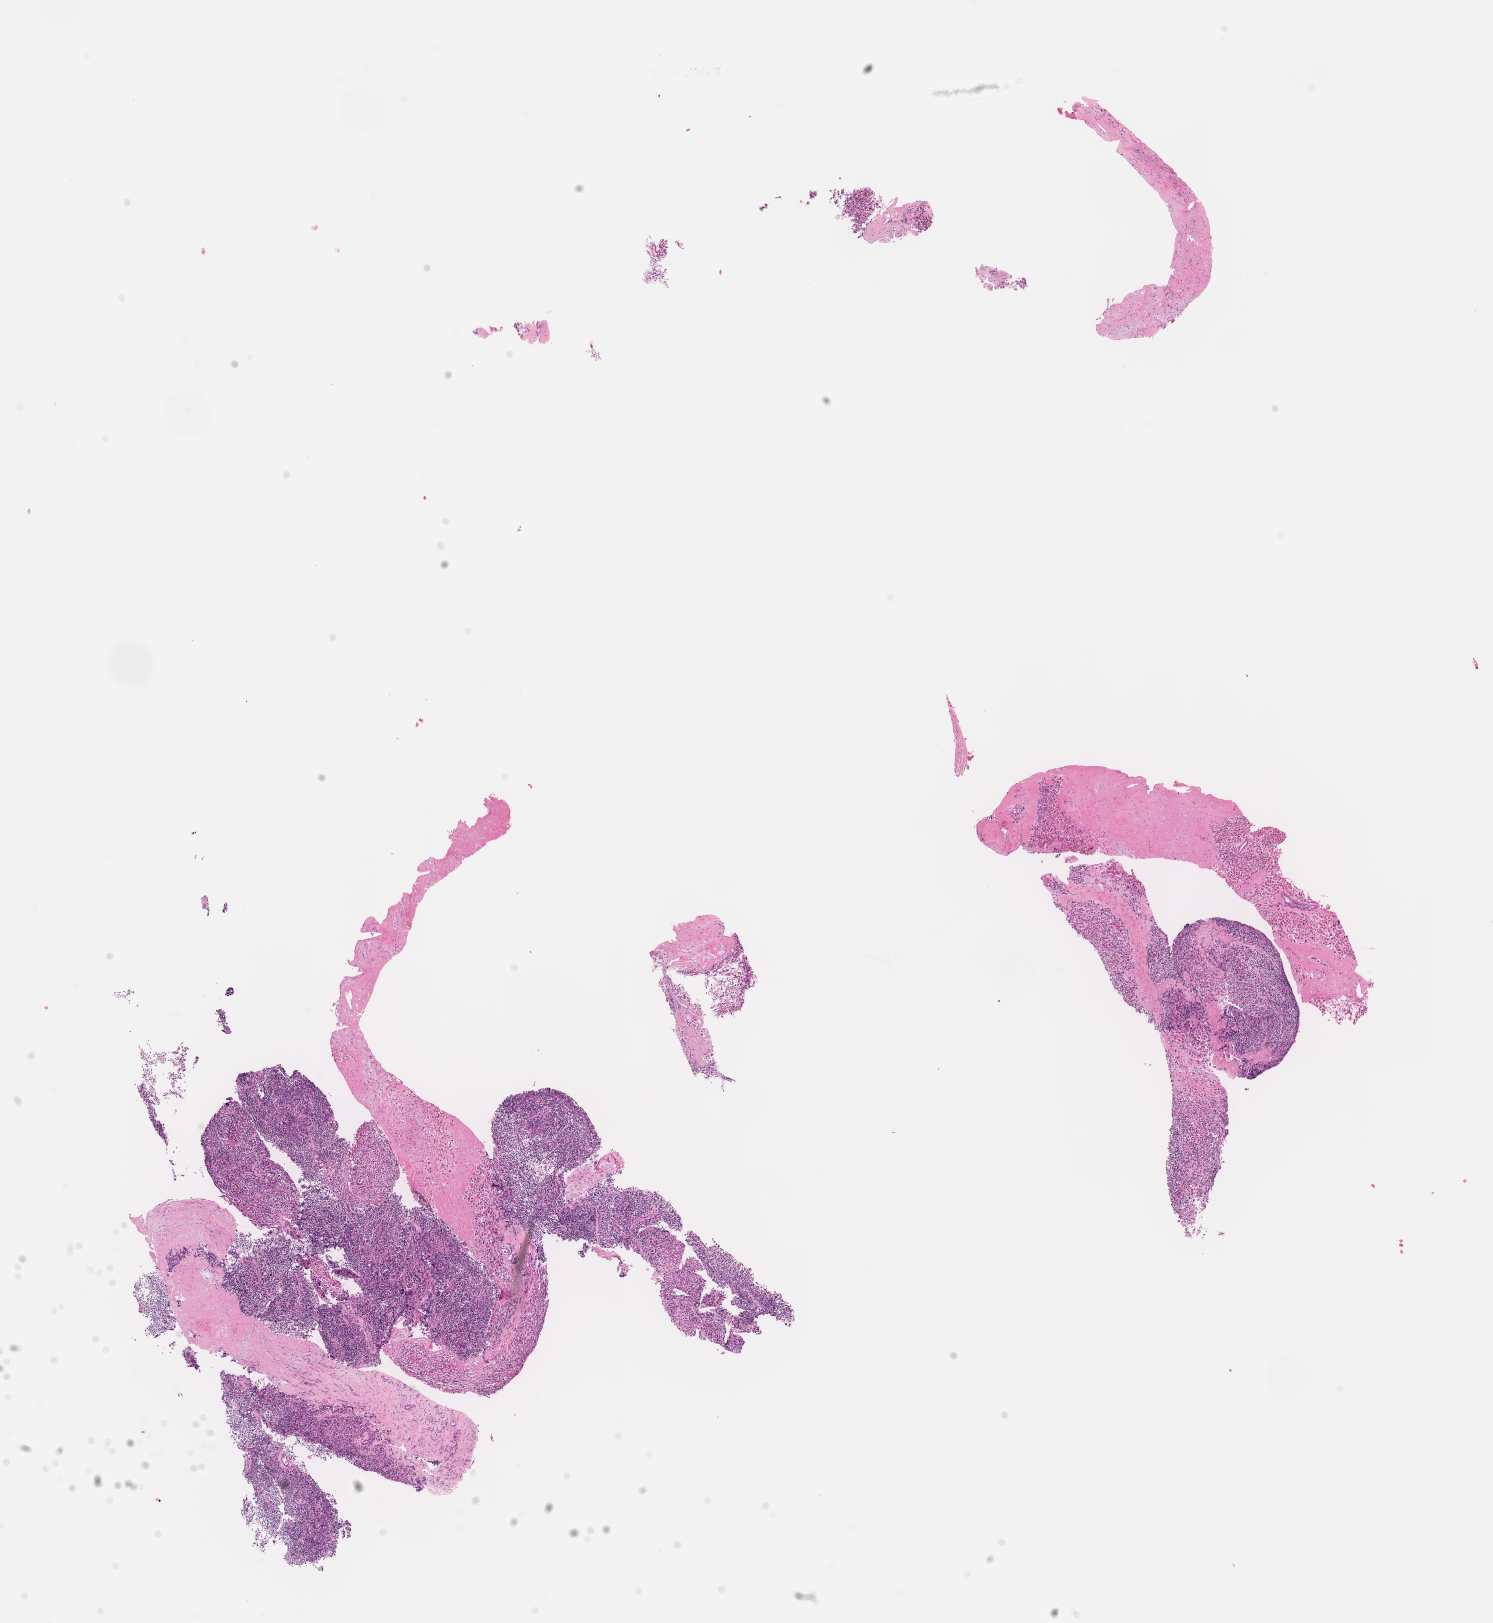
Digitized H&E-stained section of tumor tissue, a low-resolution overview of the entire scanned area, about 12.1 x 13.1 mm. FFPE section. Patient: male, age 6.9 years at diagnosis.
Diagnosis: rhabdomyosarcoma; histological classification: embryonal rhabdomyosarcoma. Metastatic status at presentation (as recorded): non-metastatic. Stage (as recorded): 3.